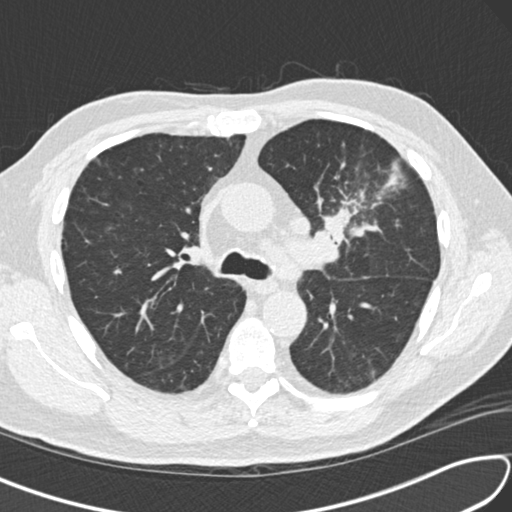
Low-dose screening chest CT, one axial slice. Slice 102 of 156 in the series (ordered by position). Lung window (W 1500 / L -600 HU). 2 mm slice thickness. 512 × 512 image matrix, field of view 340 × 340 mm.
Annotated regions visible in this slice (expert manual segmentation):
- lesion 1 (tumor, upper lobe of left lung): bounding box (x1, y1, x2, y2) in pixels: (325, 208, 353, 243)